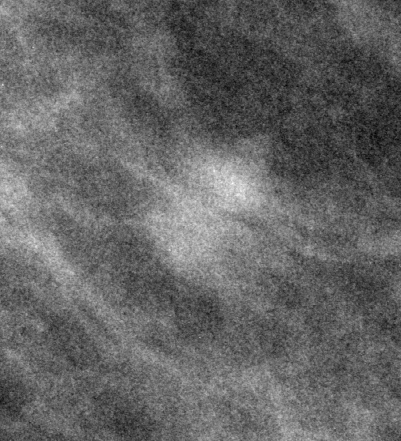
Cropped region of a digitized screen-film mammogram centred on a radiologist-marked abnormality, left breast, MLO view.
- Calcifications, morphology amorphous, distribution clustered; BI-RADS assessment category 4; subtlety rating 3 on a 1 (subtle) to 5 (obvious) scale; pathology result (as recorded, not read from the image): malignant.